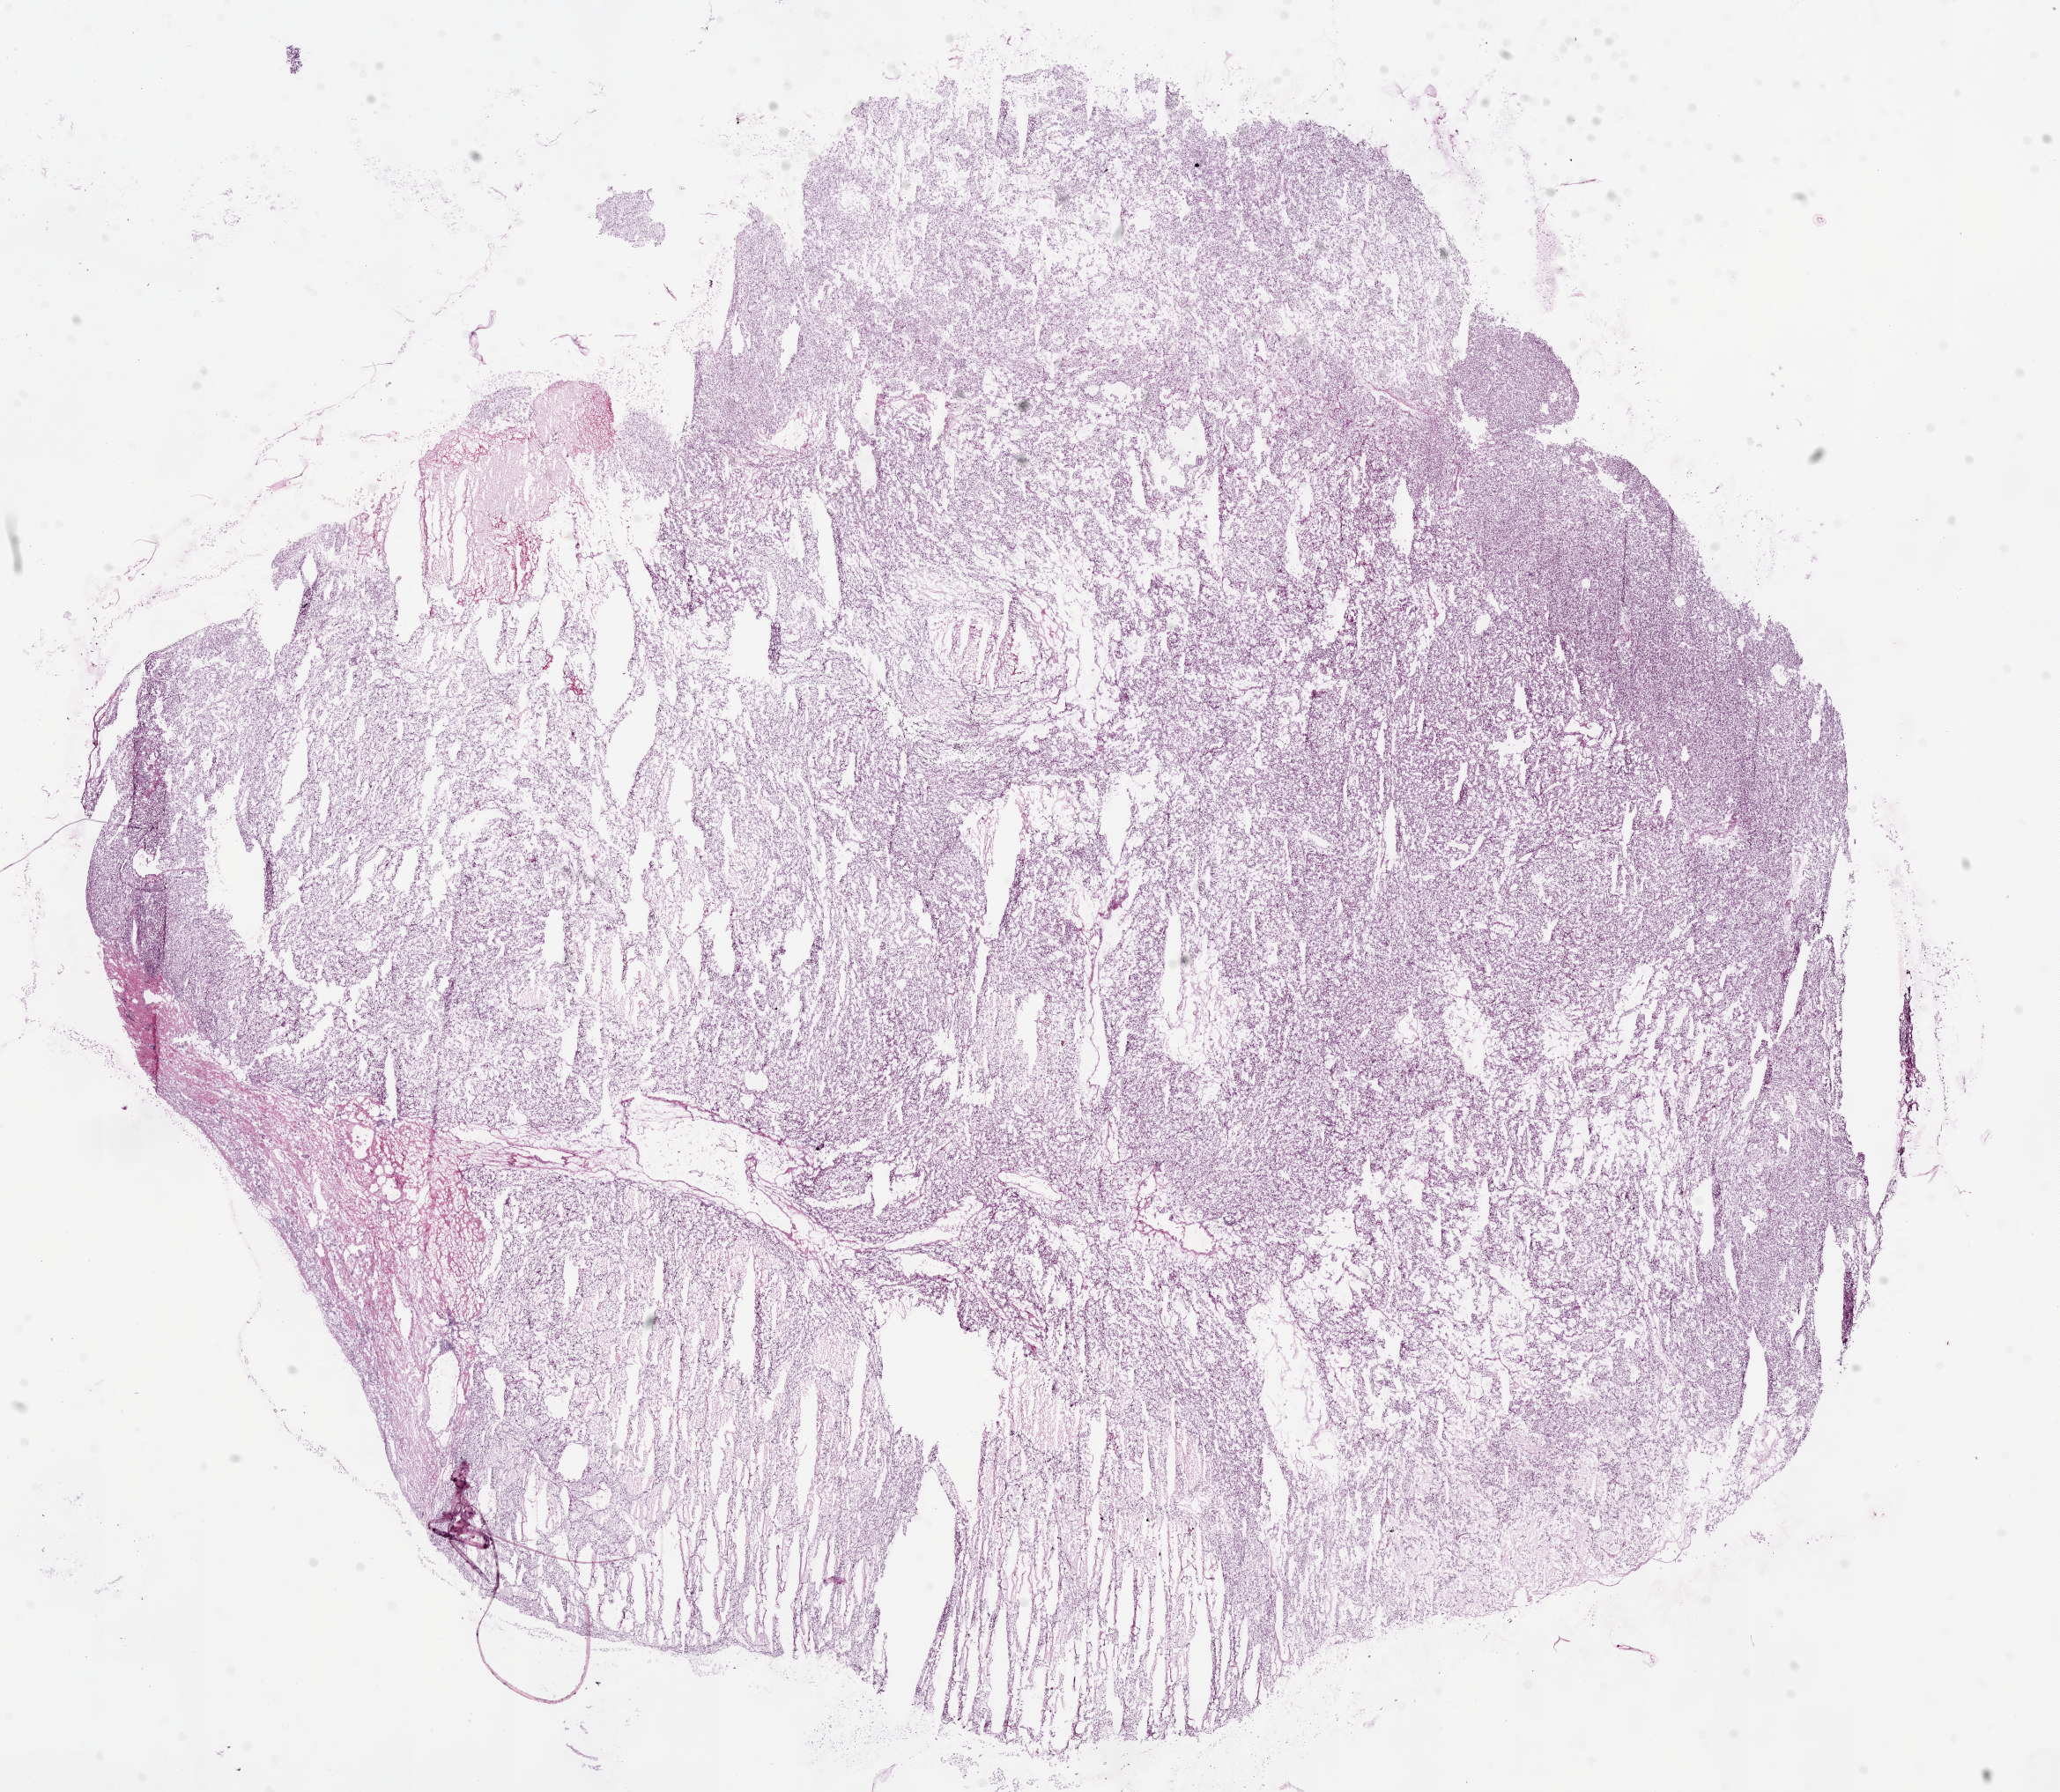
H&E whole-slide image, whole scanned area (about 18.7 x 16.3 mm) shown as a low-resolution overview; frozen section; sample: primary tumour, kidney. Female patient; age at initial diagnosis 72 years. Histologic grade: G4 (undifferentiated). Pathologist review of this section (percent, as recorded): tumour cells 95%, tumour nuclei 85%, normal cells 0%, stromal cells 5%, necrosis 0%.
Pathologic diagnosis: Clear cell adenocarcinoma, NOS. Lymph nodes positive (case pathology): 0 of 5 examined. TNM: T3a N0 M0. Laterality: left. AJCC pathologic stage: III.